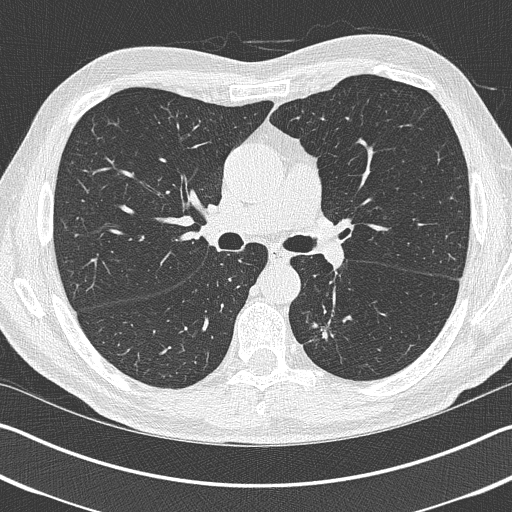
Chest CT (low-dose screening protocol), one axial image, baseline annual screen, lung window (W 1500 / L -600 HU), 1 mm slice thickness, lung (sharp) reconstruction kernel (B50f), 120 kVp. Male participant, aged 69 years at enrolment.
Lesion marked by an expert reader, bounding box (x1, y1, x2, y2) in pixels: (303, 310, 357, 360). Screening reader's record for this exam (one nodule recorded; not confirmed to be the boxed lesion): non-calcified nodule or mass ≥4 mm, left upper lobe, 19 × 19 mm, spiculated (stellate) margins, pre-existing on the prior screen: yes. Later outcome: lung cancer diagnosed 202 days after this screen — non-small cell carcinoma, left lower lobe, stage IIIA (AJCC 6th edition), 20 mm at pathology.